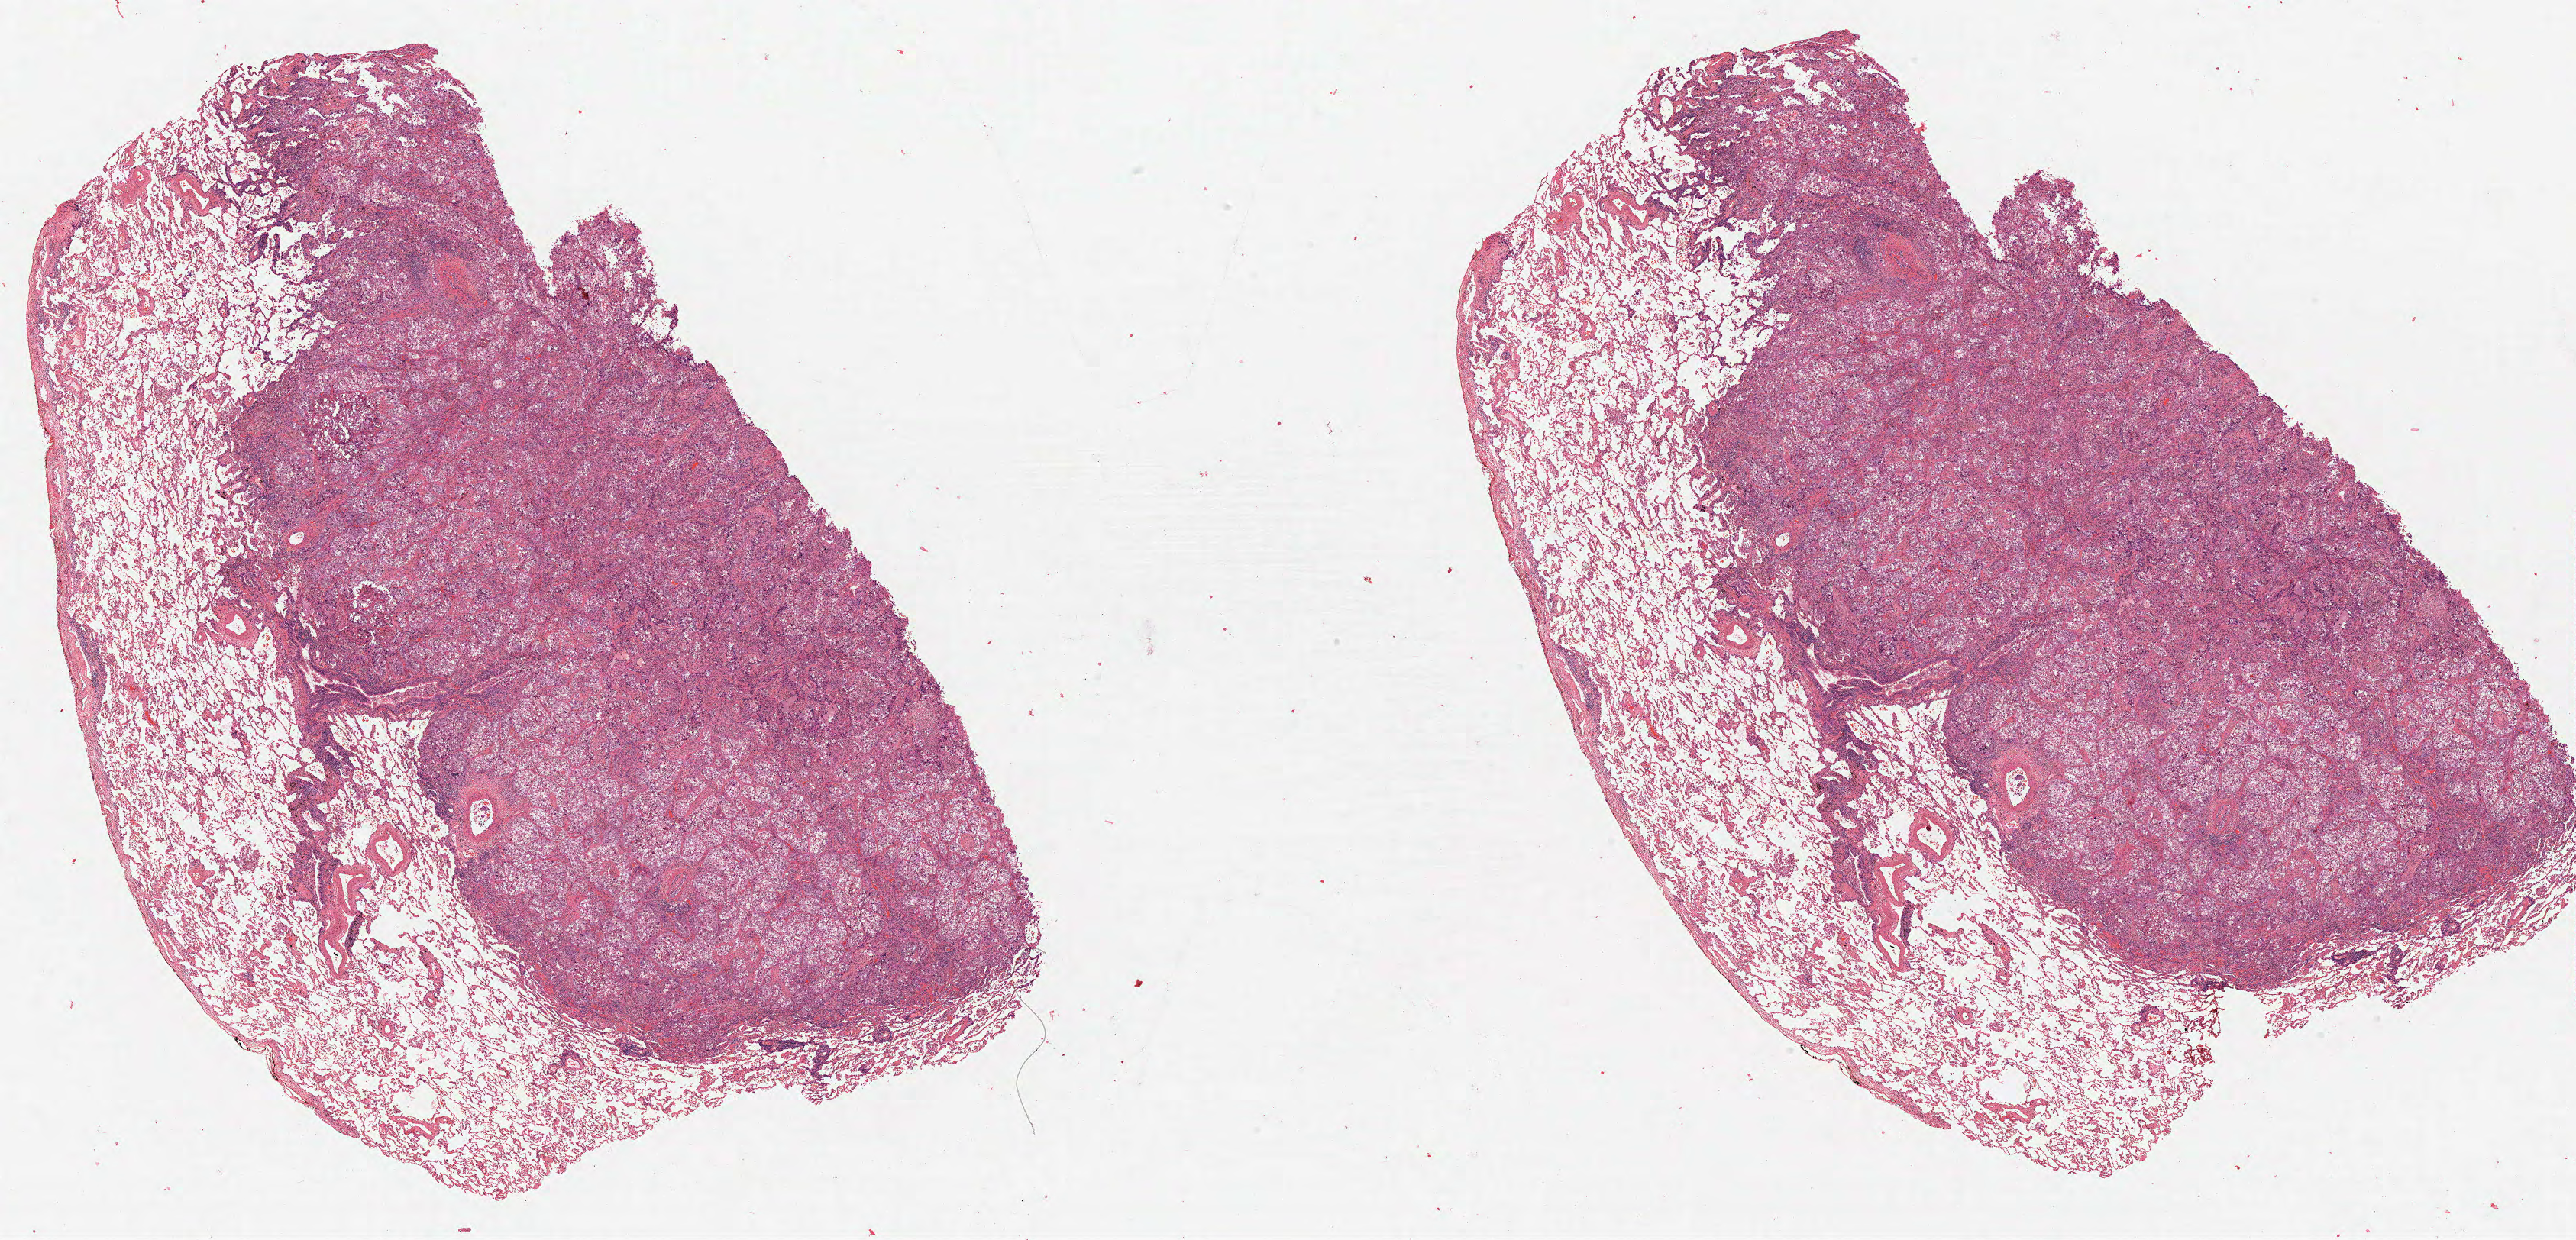
Whole-slide histology image, H&E — shown as a low-resolution overview of the whole scanned area (about 27.0 x 13.0 mm); formalin-fixed paraffin-embedded (FFPE) diagnostic section; sample: primary tumour, lung. Patient sex: male.
AJCC pathologic stage: IIA (6th edition). Histologic diagnosis: Squamous cell carcinoma, NOS.